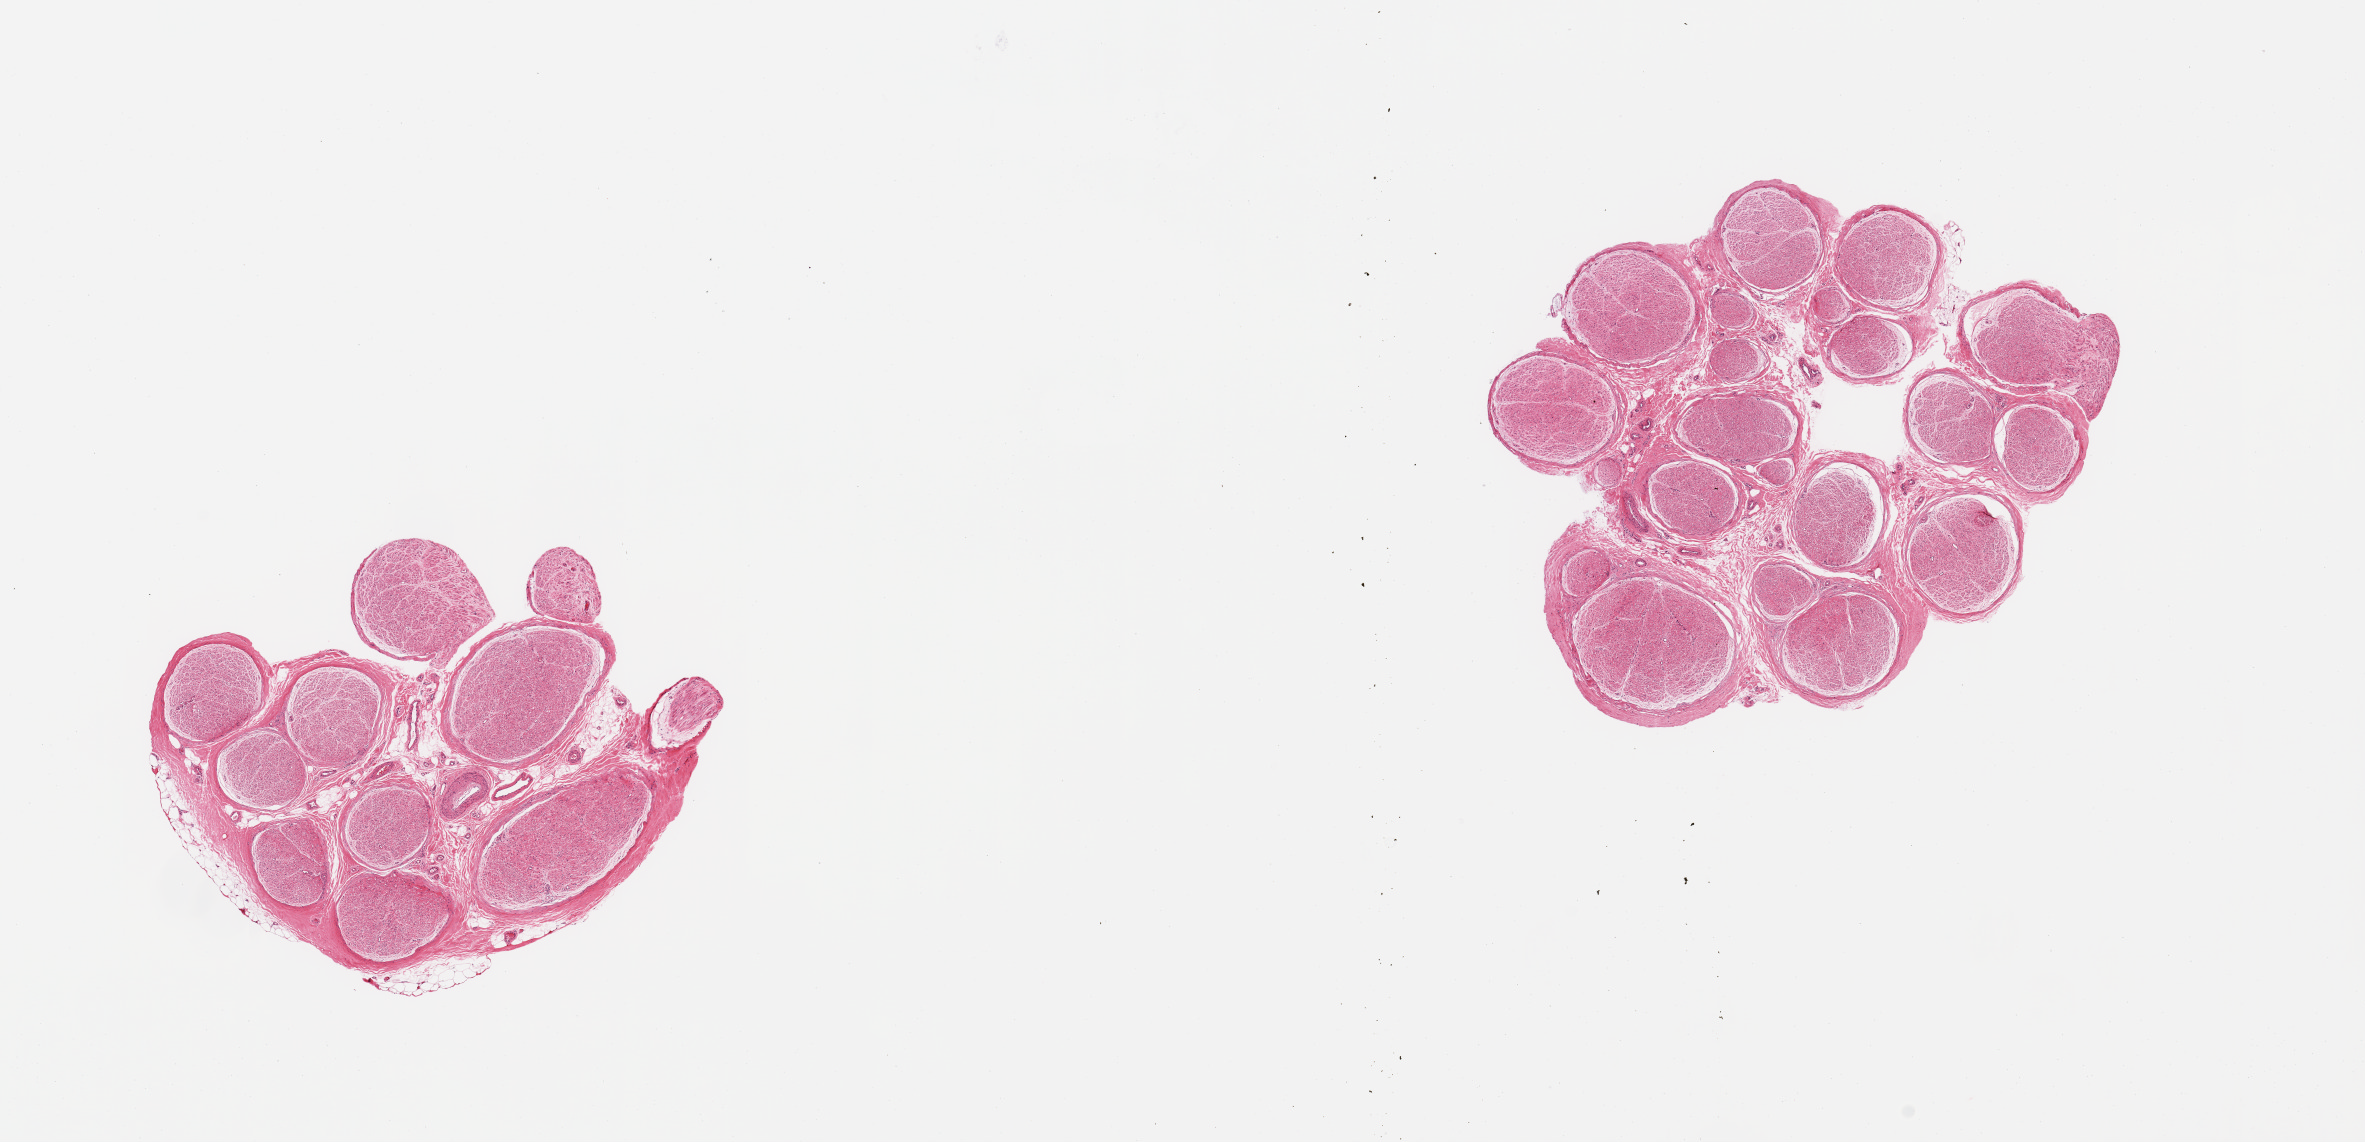
Digitized hematoxylin and eosin (H&E)-stained section, brightfield — shown as a low-resolution overview of the whole scanned area (about 18.7 x 9.0 mm, from a 20x scan); PAXgene-fixed paraffin-embedded (PFPE) section; sampled site (target tissue): tibial nerve; donor tissue sample.
Reviewer comment on this tissue sample: 2 pieces, no adherent fat.